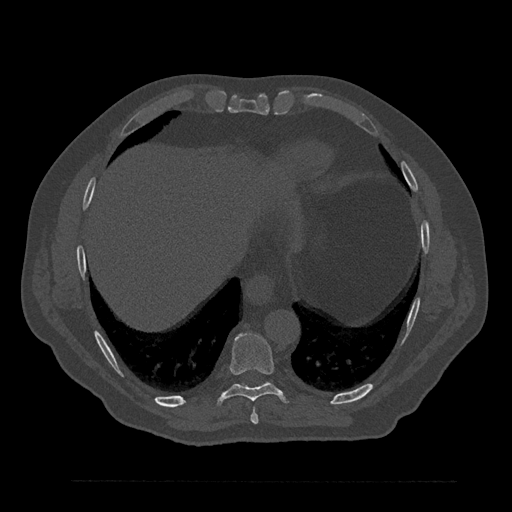
CT including the spine, one axial slice; slice 401 of 797 in the series (ordered by position); 120 kVp; bone window (W 1800 / L 400 HU); 512 × 512 image matrix. Male patient, age 61 years. Case-level facts recorded for this patient, not image findings: primary cancer: prostate.
Outlined on this slice (semi-automatically segmented with operator editing):
- T8 vertebra: box from (x=250, y=409) to (x=259, y=424) px
- T9 vertebra: (x=217, y=333)–(x=287, y=406)